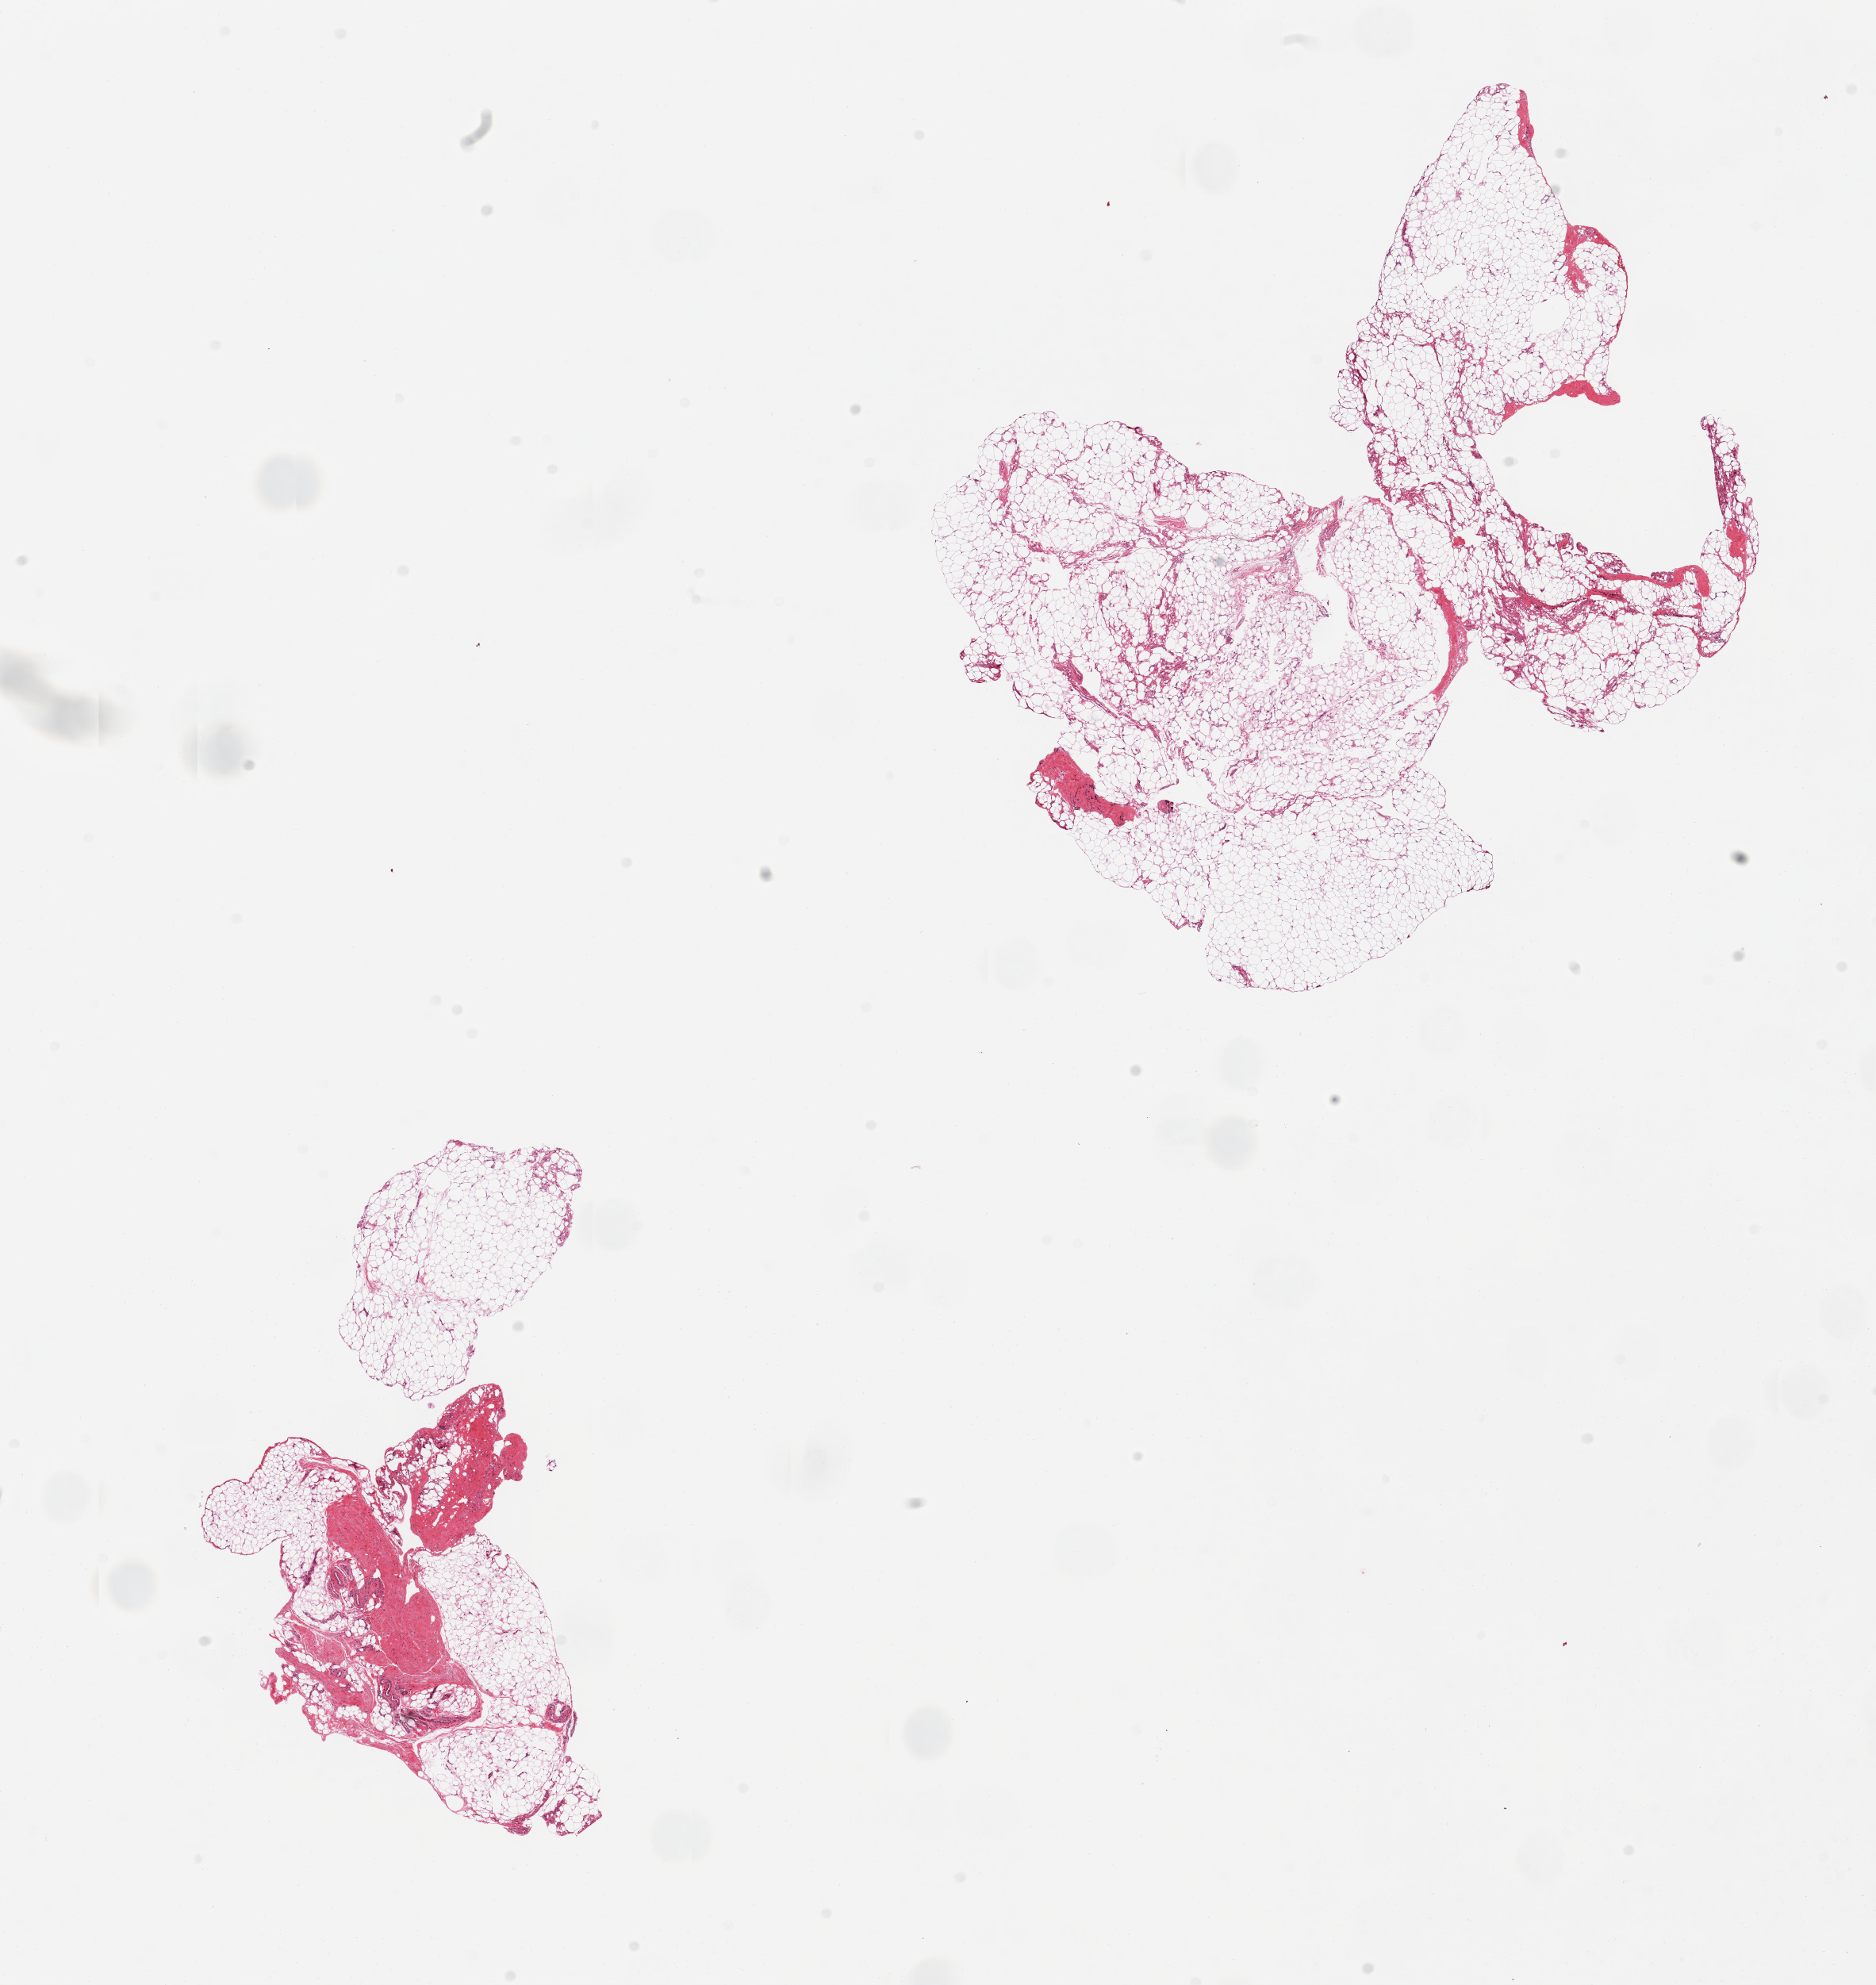
Digitized H&E-stained section — low-resolution overview of the scanned area, about 18.7 x 19.8 mm, PAXgene-fixed, paraffin-embedded tissue, sampled site (target tissue): adipose tissue, tissue donor sample. Donor: female.
Review note (as recorded): 2 pieces; smaller piece has 20% fibrous tissue.